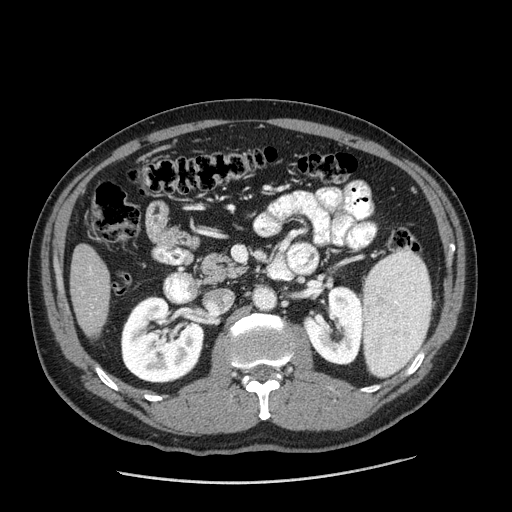
Contrast-enhanced abdominal CT (liver protocol), one axial slice; slice 61 of 198 in the series (ordered by position); one of 2 acquisitions stored at this slice position; soft-tissue window (W 400 / L 40 HU); 512 × 512 image matrix, field of view 400 × 400 mm. Case-level facts recorded for this patient, not image findings: diagnosis: hepatocellular carcinoma (patient treated with transarterial chemoembolisation; whether this scan precedes or follows treatment is not stated here); TNM stage (as recorded): Stage-II; Child-Pugh class: A; tumour differentiation: moderately differentiated.
Structures marked on this image (semi-automatic segmentation, software-assisted and operator-edited):
- liver parenchyma outside the tumour (the mass and vessels are separate outlines, so this box may not span the whole liver): bounding box [x1, y1, x2, y2] px = [70, 244, 110, 336]